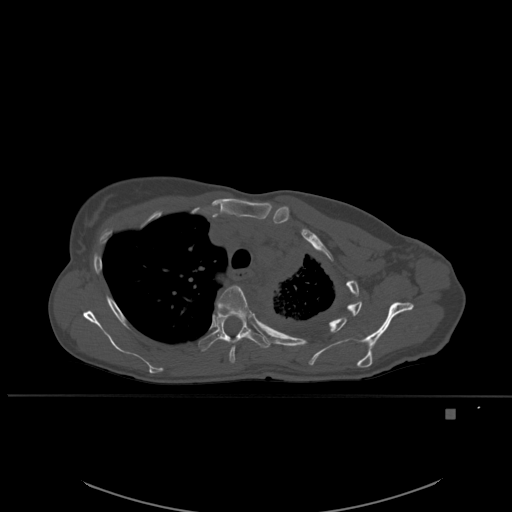
CT including the spine, one axial slice. Slice 405 of 537 in the series (ordered by position). Bone window (W 1800 / L 400 HU). 512 × 512 image matrix, field of view 440 × 440 mm. Patient: female, 45 years. From the clinical record (not read from this slice): primary cancer: lung.
Structures marked on this image (semi-automatic segmentation, software-assisted and operator-edited):
- T4 vertebra: bounding box (x1, y1, x2, y2) in pixels: (216, 285, 251, 364)
- T5 vertebra: (199, 310, 270, 351)